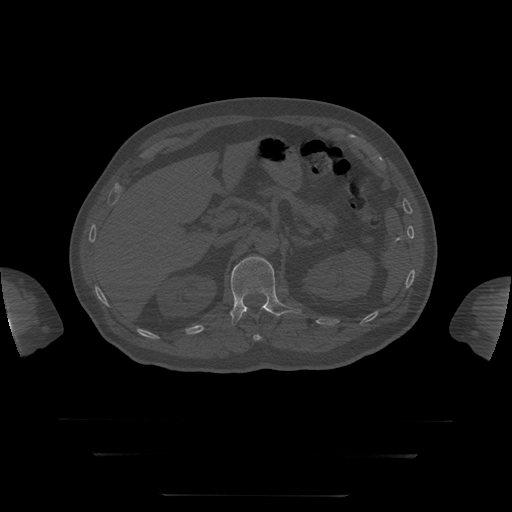
CT including the spine, one axial slice. Slice 55 of 397 in the series (ordered by position). Reconstruction kernel STANDARD. 120 kVp. Bone window (W 1800 / L 400 HU). 1.25 mm slice thickness. 512 × 512 image matrix, field of view 510 × 510 mm. Patient age 73 years. Case-level facts recorded for this patient, not image findings: primary cancer: prostate.
Outlined on this slice (semi-automatic segmentation, software-assisted and operator-edited):
- L1 vertebra: bounding box (x1, y1, x2, y2) in pixels: (231, 257, 301, 325)
- T12 vertebra: (253, 335, 262, 341)
- T8 vertebra: (240, 298, 273, 319)